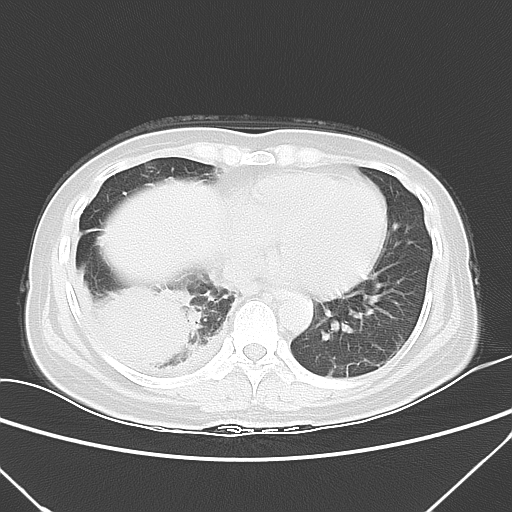
Chest CT, one axial slice; position 15 of 53 along the scan axis; 120 kVp; lung window (W 1500 / L -600 HU); 512 × 512 image matrix, field of view 337 × 337 mm. Patient: female, 42 years. From the clinical record (not read from this slice): clinical TNM (as recorded): T3 N0 M1c.
Annotated regions visible in this slice (rectangle marked by the reading radiologist):
- lung tumour (recorded histology: adenocarcinoma): bounding box [x1, y1, x2, y2] px = [93, 280, 195, 369]